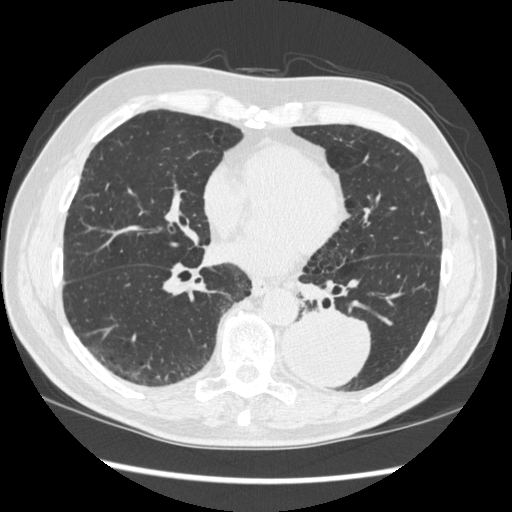
Chest CT (low-dose screening protocol), one axial image, first (baseline) screen, lung window (W 1500 / L -600 HU), standard (soft-tissue) reconstruction kernel (STANDARD), slice 141 of 348 in the series, 512 × 512 image matrix, field of view 360 × 360 mm. Male participant, aged 72 years at enrolment. Current smoker at enrolment.
- Expert reader's lesion annotation, box from (x=269, y=301) to (x=373, y=391) px.
- The screening reader recorded 2 non-calcified nodules or masses ≥4 mm on this exam (left lower lobe, right middle lobe); which of them this box marks is not recorded.
- Later outcome: lung cancer diagnosed 37 days after this screen — squamous cell carcinoma, NOS, left lower lobe, stage IIIA (AJCC 6th edition), 60 mm at pathology.